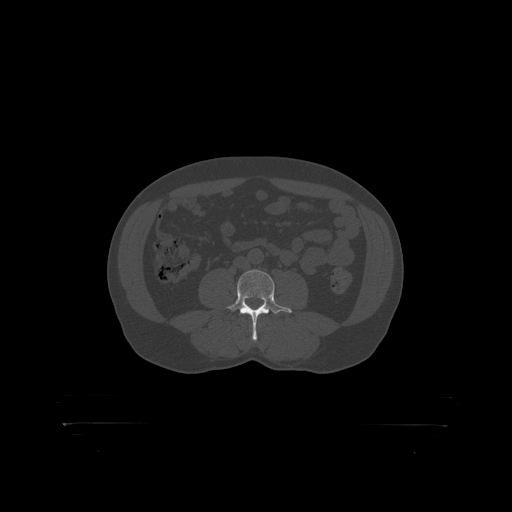
CT including the spine, one axial slice. Position 239 of 399 along the scan axis. Reconstruction kernel STANDARD. Bone window (W 1800 / L 400 HU). 1.25 mm slice thickness. 512 × 512 image matrix. Male patient, age 46 years. Case-level facts recorded for this patient, not image findings: primary cancer: skin.
Annotated regions visible in this slice (semi-automatically segmented with operator editing):
- L4 vertebra: bounding box [x1, y1, x2, y2] px = [226, 270, 290, 319]